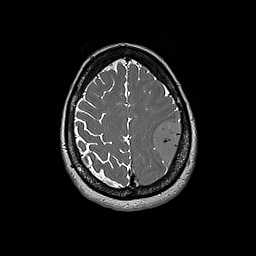
Brain MRI from a brain-tumour surgery series, one axial slice. Slice 57 of 192 in the series (ordered by position). 1 mm slice thickness. 256 × 256 image matrix, field of view 250 × 250 mm. Case-level facts recorded for this patient, not image findings: histopathology: Glioblastoma; WHO grade: 4.
Outlined on this slice (manually delineated by an expert):
- tumour: box from (x=152, y=117) to (x=183, y=166) px